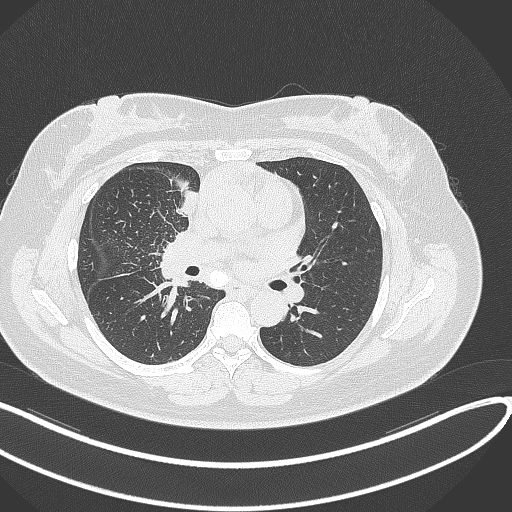
Chest CT, one axial slice; slice 144 of 303 in the series (ordered by position); 120 kVp; lung window (W 1500 / L -600 HU); 512 × 512 image matrix, field of view 400 × 400 mm. Female patient, age 46 years. Case-level facts recorded for this patient, not image findings: clinical TNM (as recorded): T2a N1 M0.
Structures marked on this image (bounding box drawn by a radiologist):
- lung tumour (recorded histology: adenocarcinoma): box from (x=174, y=192) to (x=198, y=218) px